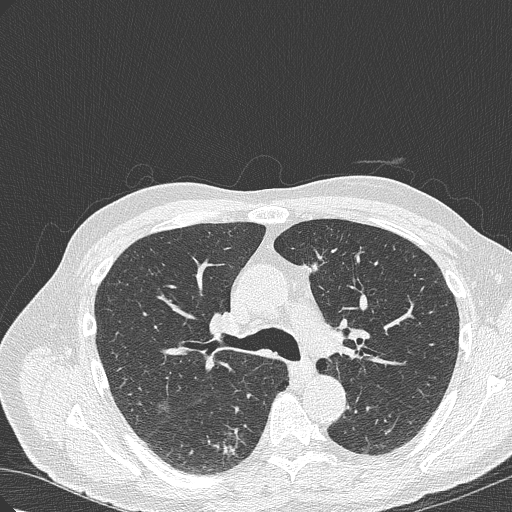
Chest CT (low-dose screening protocol), one axial image; first (baseline) screen; lung window (W 1500 / L -600 HU); lung (sharp) reconstruction kernel (B50f); 120 kVp; slice 111 of 322 in the series. Male, age 70 years at enrolment. Current smoker at enrolment.
• Expert-annotated lung lesion, bounding box (x1, y1, x2, y2) in pixels: (201, 419, 265, 466).
• The screening reader recorded 4 non-calcified nodules or masses ≥4 mm on this exam (right lower lobe, right lower lobe, right upper lobe, right lower lobe); which of them this box marks is not recorded.
• Later outcome: lung cancer diagnosed 978 days after this screen (after the third annual screen) — bronchiolo-alveolar adenocarcinoma, NOS, right lower lobe, poorly differentiated (G3), stage IB (AJCC 6th edition), 30 mm at pathology.